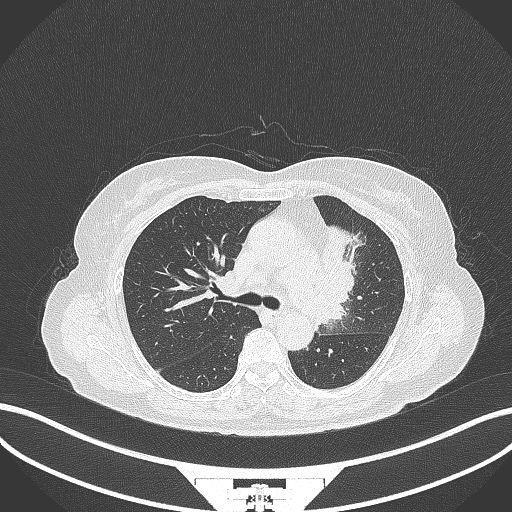
Chest CT, one axial slice. Position 216 of 382 along the scan axis. 120 kVp. Lung window (W 1500 / L -600 HU). 1 mm slice thickness. 512 × 512 image matrix. Patient: female, 64 years. From the clinical record (not read from this slice): clinical TNM (as recorded): T2a N2 M0.
Structures marked on this image (rectangle marked by the reading radiologist):
- lung tumour (recorded histology: adenocarcinoma): bounding box <319,222,353,328> (left, top, right, bottom; pixels)